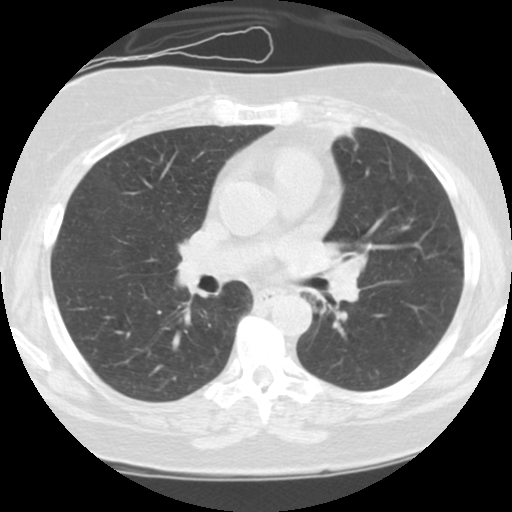
Low-dose screening chest CT, axial slice, third screening round (two years after baseline), lung window (W 1500 / L -600 HU), standard (soft-tissue) reconstruction kernel (STANDARD), 120 kVp, slice 48 of 108 in the series. Female, age 59 years at enrolment. Current smoker at enrolment.
Expert-annotated lung lesion, box from (x=285, y=213) to (x=390, y=325) px. Screening reader's record for this exam: no non-calcified nodule ≥4 mm recorded. Official screen result: positive, other. Lung cancer was diagnosed 192 days after this screen: small cell carcinoma, NOS, left upper lobe, left hilum, mediastinum, left main stem bronchus, stage IV (AJCC 6th edition), 63 mm at pathology.